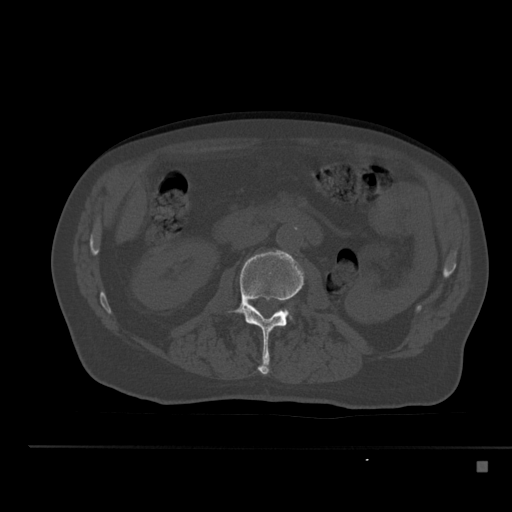
CT including the spine, one axial slice. Reconstruction kernel Br40s. 120 kVp. Bone window (W 1800 / L 400 HU). 512 × 512 image matrix, field of view 408 × 408 mm. Male patient, age 70 years. From the clinical record (not read from this slice): primary cancer: renal.
Outlined on this slice (semi-automatically segmented with operator editing):
- L2 vertebra: bounding box (x1, y1, x2, y2) in pixels: (228, 250, 304, 375)